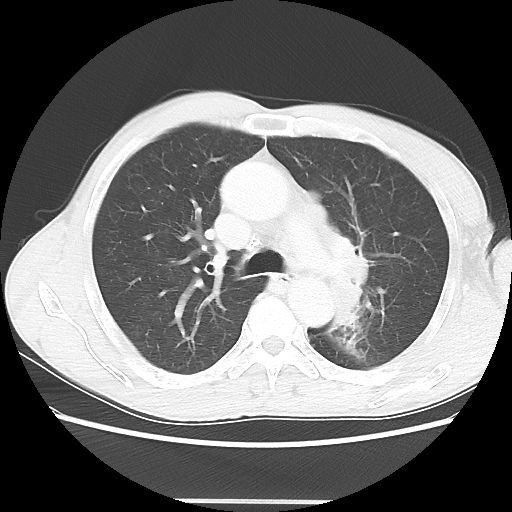
Chest CT, one axial slice. Position 43 of 62 along the scan axis. Reconstruction kernel LUNG. 100 kVp. Lung window (W 1500 / L -600 HU). 5 mm slice thickness. 512 × 512 image matrix, field of view 360 × 360 mm. Patient: male, 61 years. Case-level facts recorded for this patient, not image findings: clinical TNM (as recorded): T3 N1 M1.
Annotated regions visible in this slice (bounding box drawn by a radiologist):
- lung tumour (recorded histology: adenocarcinoma): box from (x=302, y=188) to (x=370, y=340) px